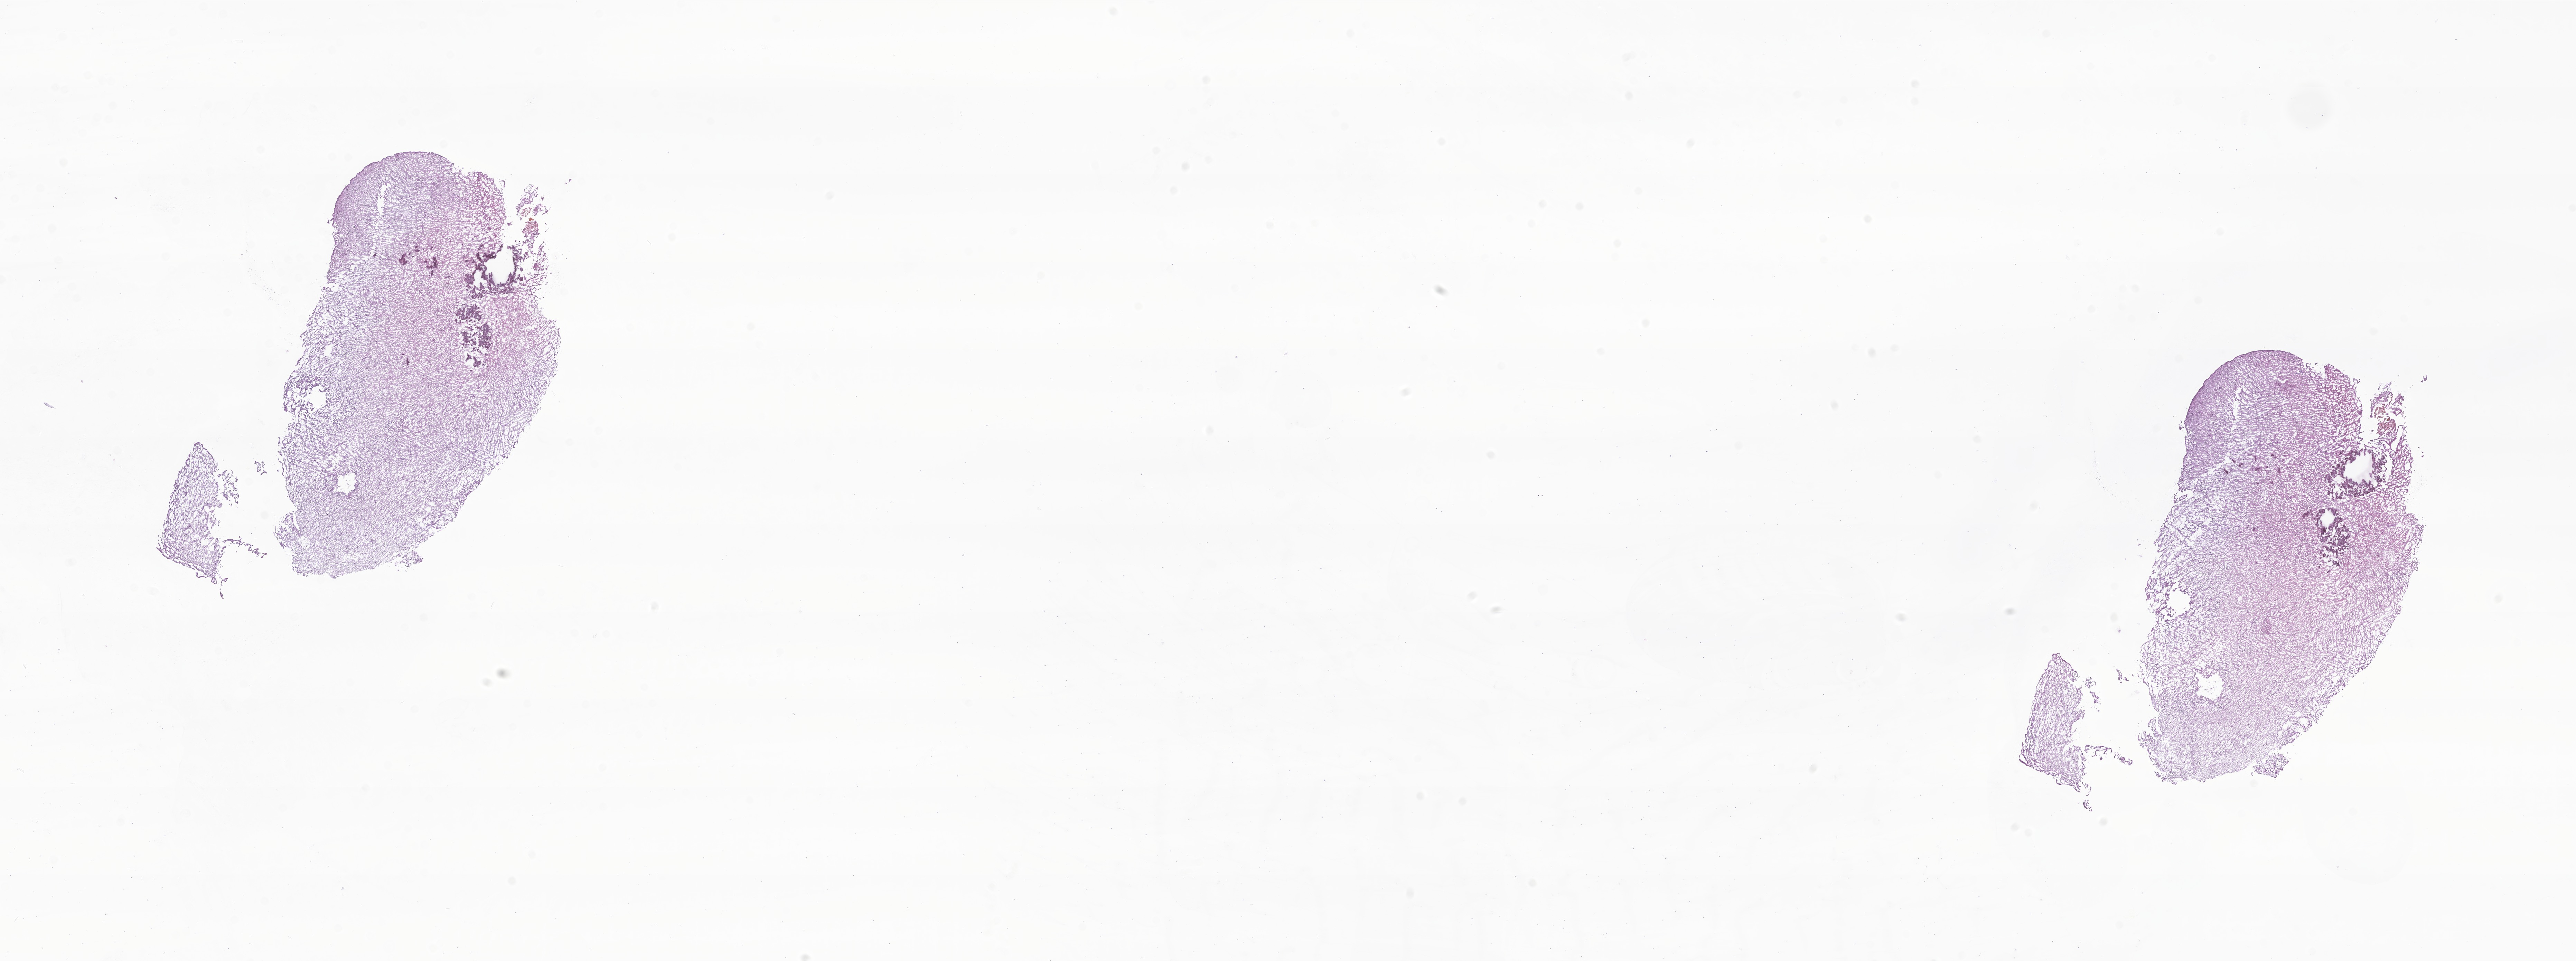
Digitized haematoxylin and eosin-stained section of tumor tissue from the brain — shown as a low-resolution overview of the whole scanned area (about 31.4 x 11.7 mm). Frozen section (OCT-embedded). Patient male; age 736 days (about 2.0 years).
• recorded diagnosis: Neoplasm, malignant